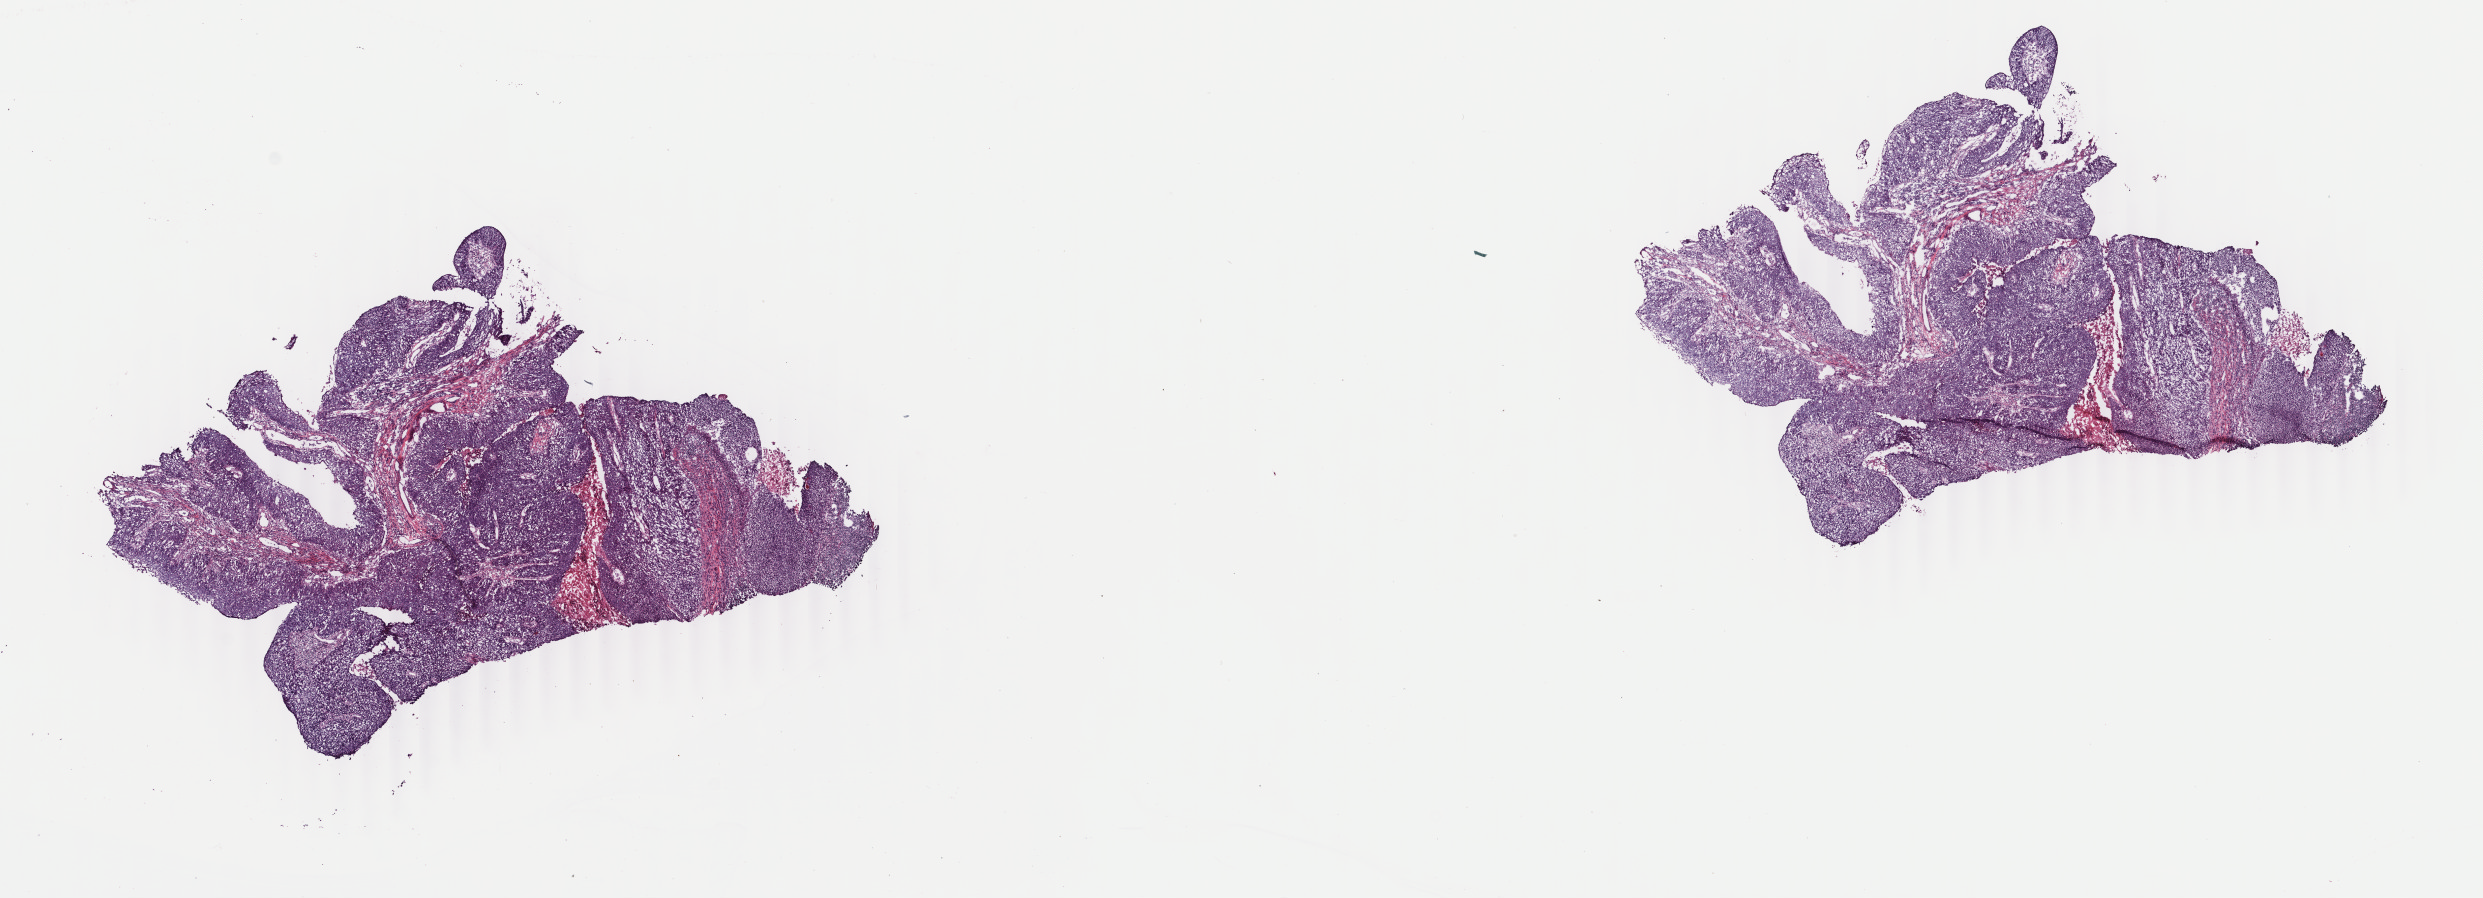
Digitized H&E-stained tissue section (whole slide) — shown as a low-resolution overview of the whole scanned area (about 19.8 x 7.1 mm); frozen section from the top of the tissue portion; primary tumour sample from the head and neck. Patient: male, age at initial diagnosis 58 years. Histologic grade: G3 (poorly differentiated). Pathologist review of this section (percent, as recorded): tumour cells 75%, tumour nuclei 80%, normal cells 0%, stromal cells 20%, necrosis 5%. Infiltration values recorded for this section: lymphocyte infiltration 10%, monocyte infiltration 2%, neutrophil infiltration 3%.
Diagnosis: Squamous cell carcinoma, large cell, nonkeratinizing, NOS (tonsil, NOS). TNM: T2 N0 M0. AJCC pathologic stage: II (7th edition).